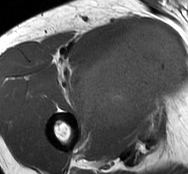
MRI of an extremity soft-tissue mass, one axial slice; MR volume resampled by the dataset authors to the PET/CT grid (not the native acquisition matrix); 188 × 174 image matrix, field of view 184 × 170 mm. Male patient. Case-level facts recorded for this patient, not image findings: histological type: undifferentiated - pleiomorphic; grade: high; site of the primary tumour: right thigh.
Annotated regions visible in this slice (expert contour drawn on MRI and transferred to this co-registered scan by the dataset authors):
- gross tumour volume including surrounding oedema: bounding box <75,23,185,129> (left, top, right, bottom; pixels)
- gross tumour volume (mass): <75,23,185,129>